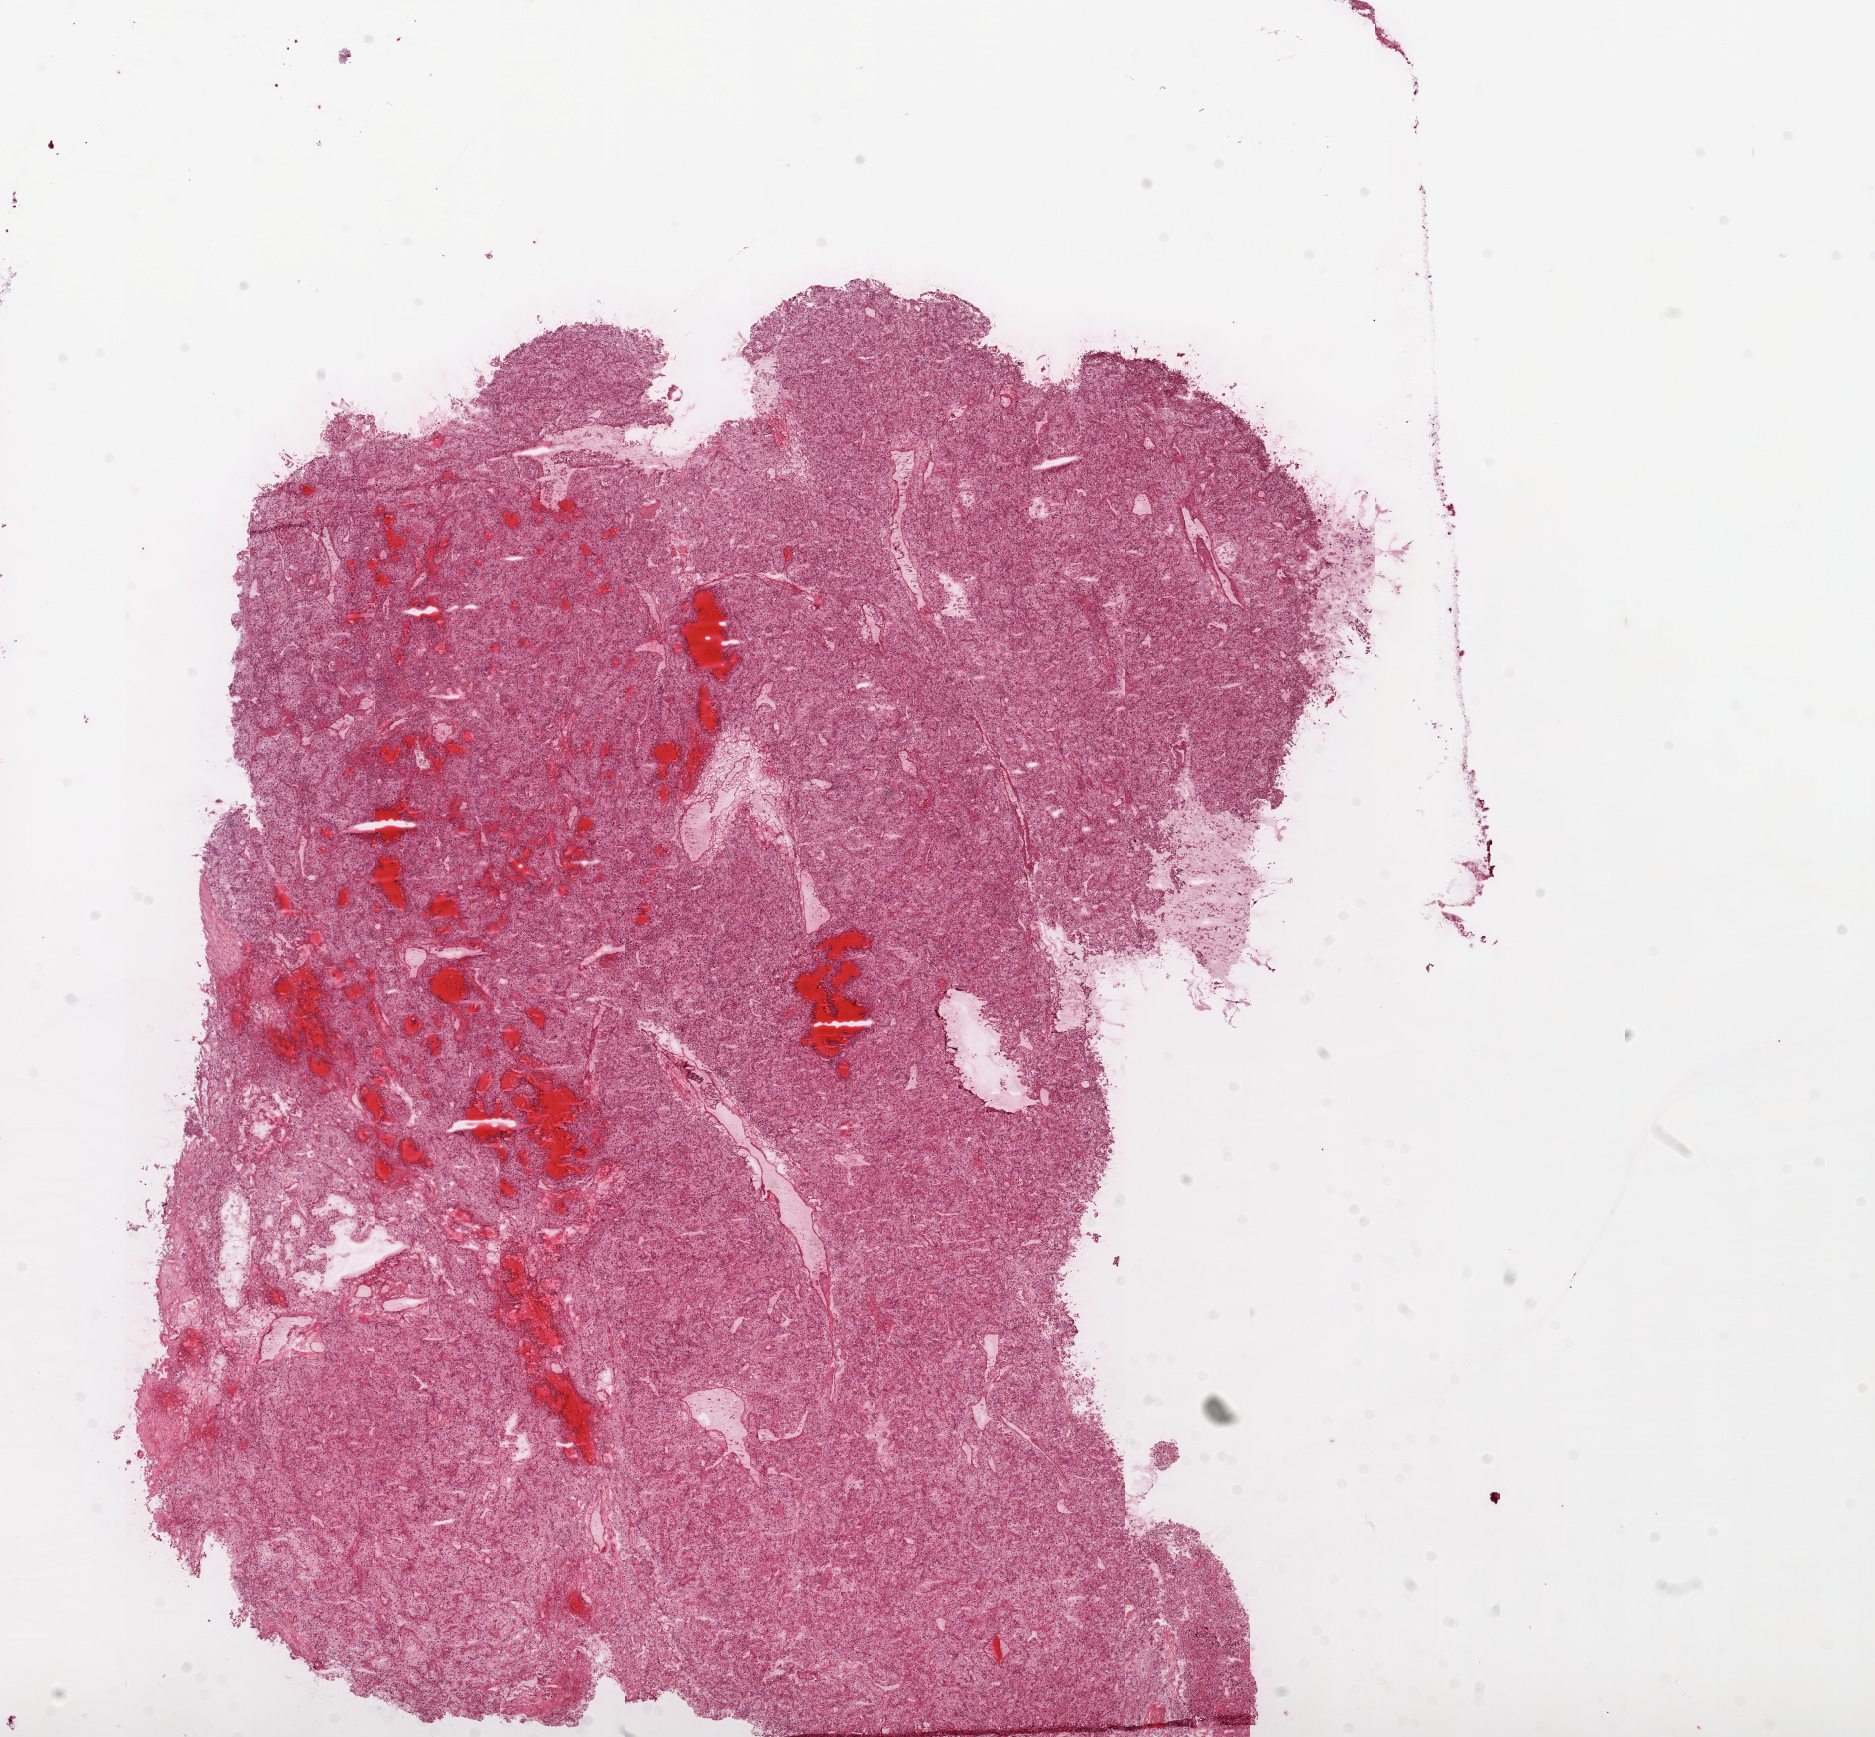
Hematoxylin and eosin (H&E) stained whole-slide image, whole scanned area (about 15.0 x 13.9 mm, slide scanned at 20x) shown as a low-resolution overview. Frozen section from the top of the tissue portion. Sample: primary tumour, kidney. Male patient; age at initial diagnosis 63 years. Histologic grade: G3 (poorly differentiated). Composition of this section per pathologist review: tumour cells 90%, tumour nuclei 85%, normal cells 0%, stromal cells 10%, necrosis 0%.
* AJCC pathologic stage: I
* pathologic diagnosis: Clear cell adenocarcinoma, NOS